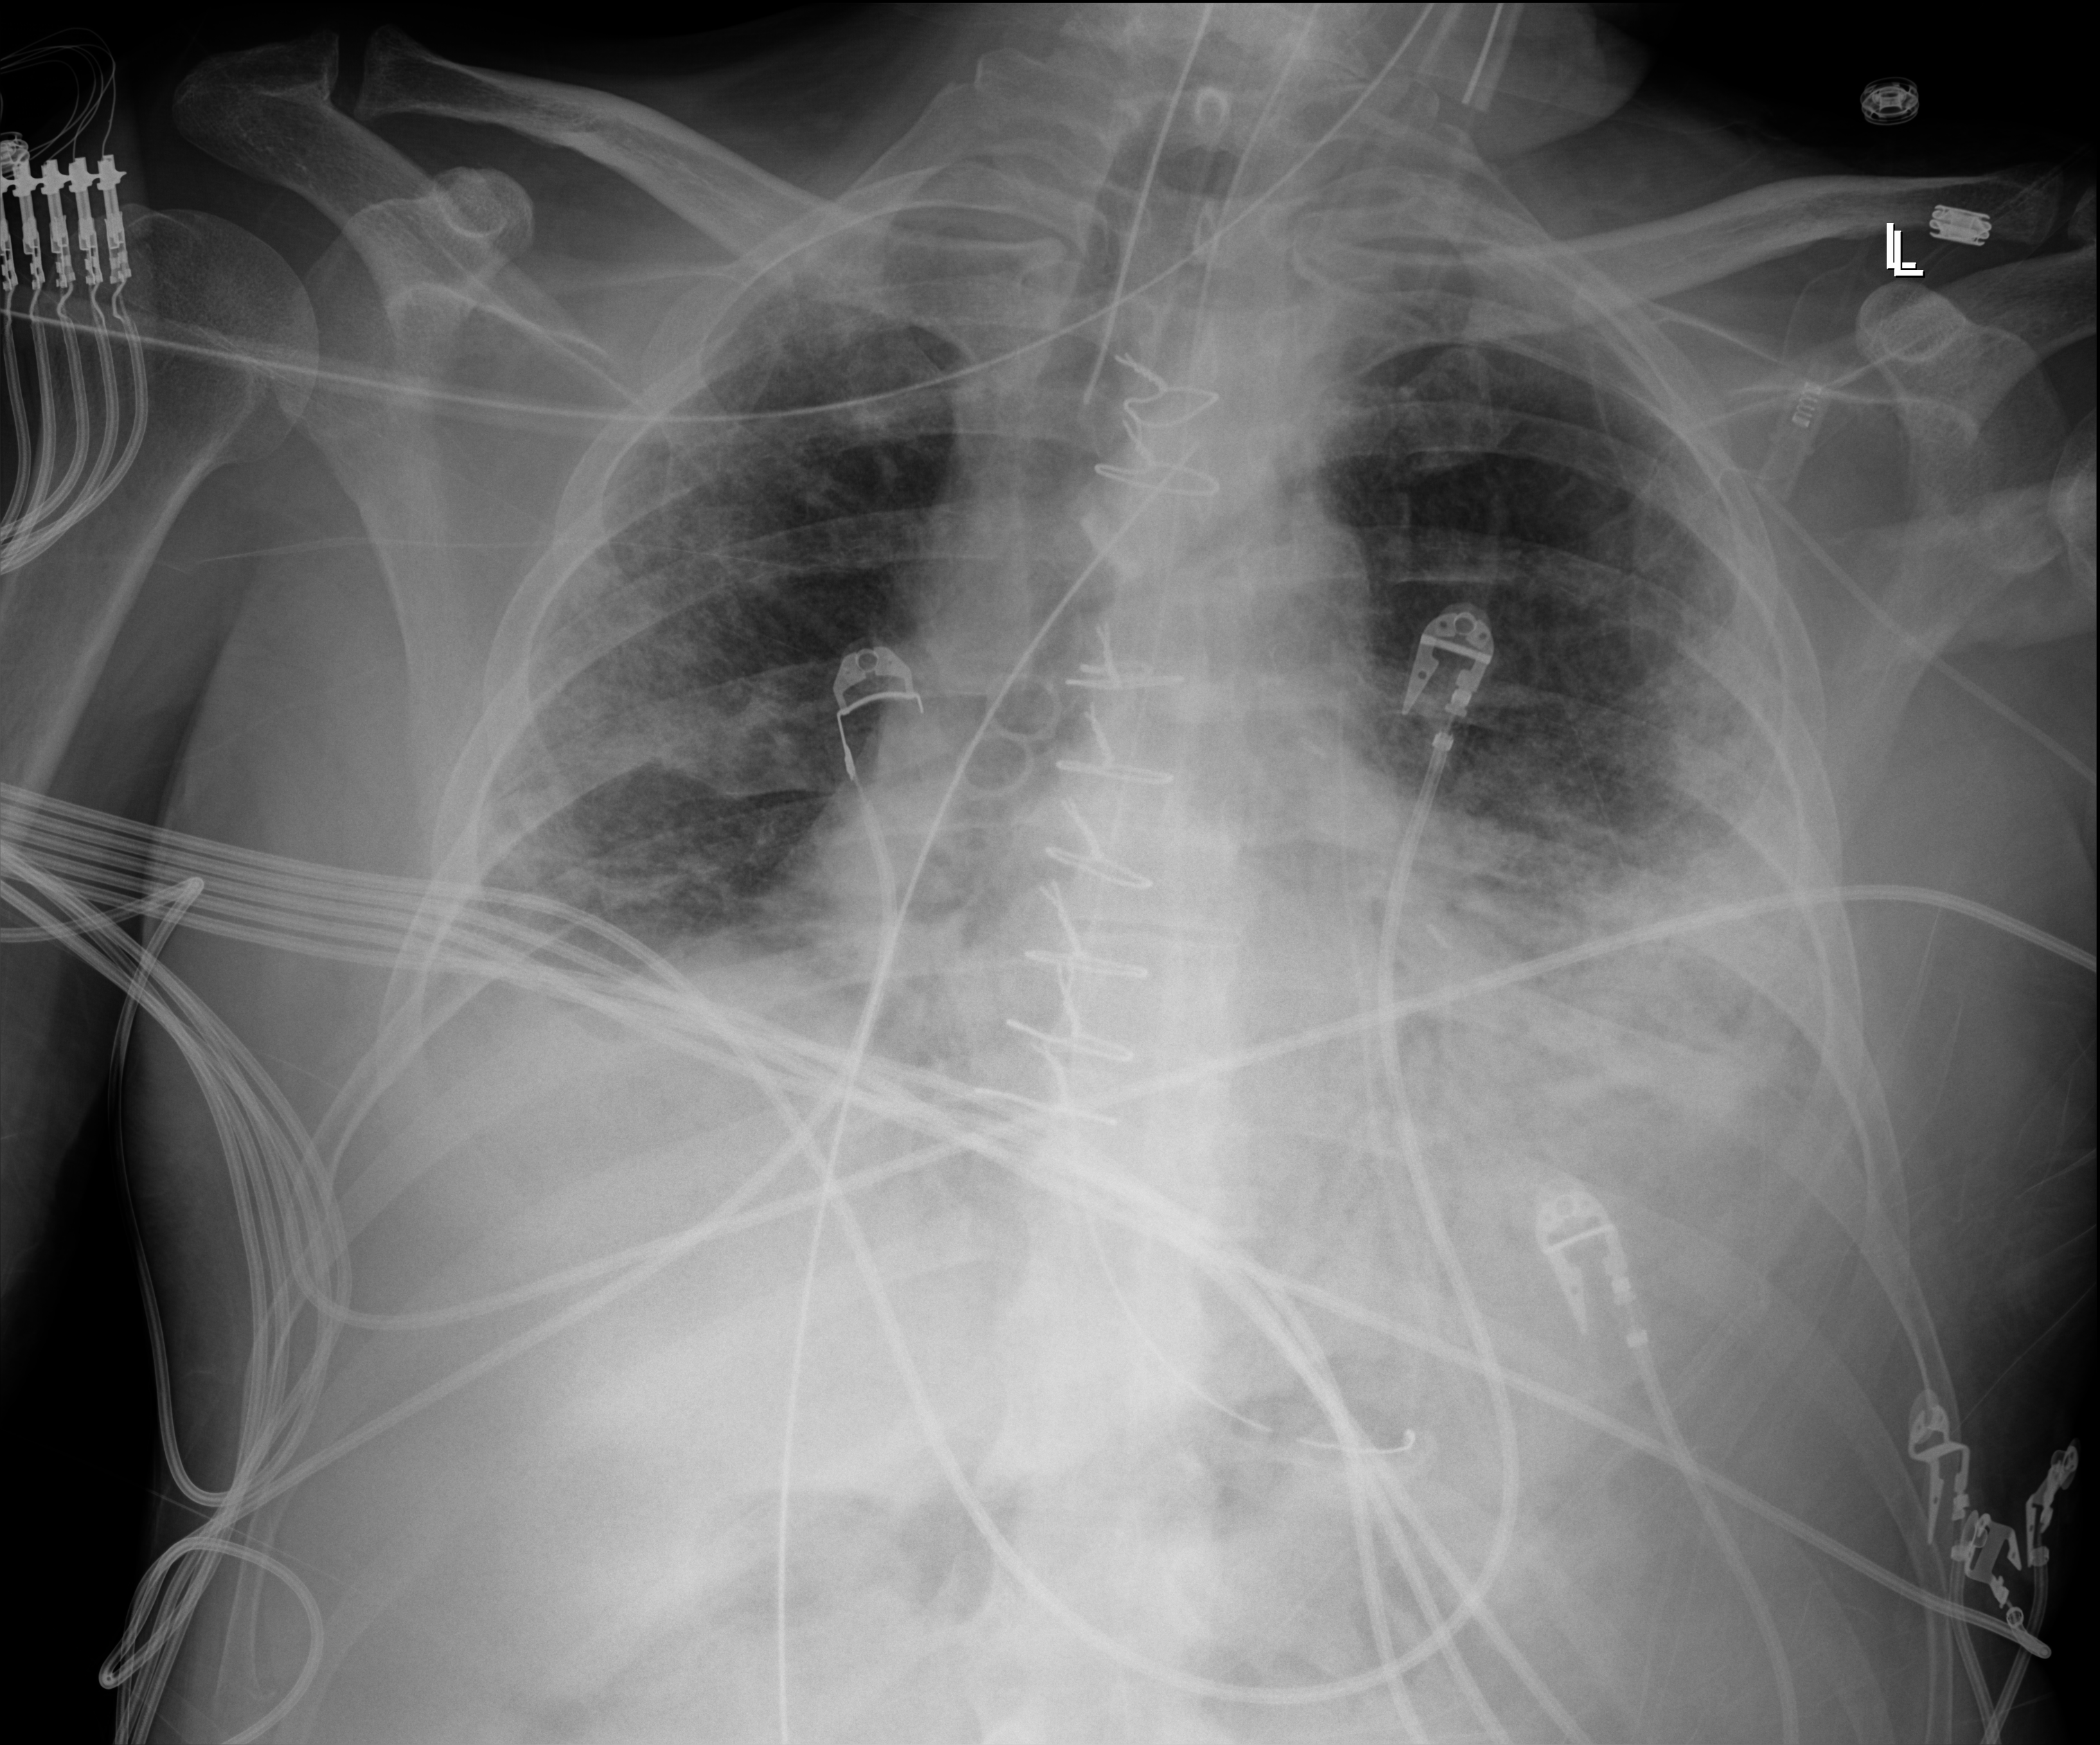
Bedside chest radiograph (digital radiography), anteroposterior (AP) projection. Male patient hospitalised with COVID-19, age 18–59 years.
Hospital-stay facts (about this admission, not read from this image; timing relative to this image not recorded): admitted to intensive care during this hospital stay: yes; hypertension (admission record): no; mechanically ventilated during this hospital stay: yes.